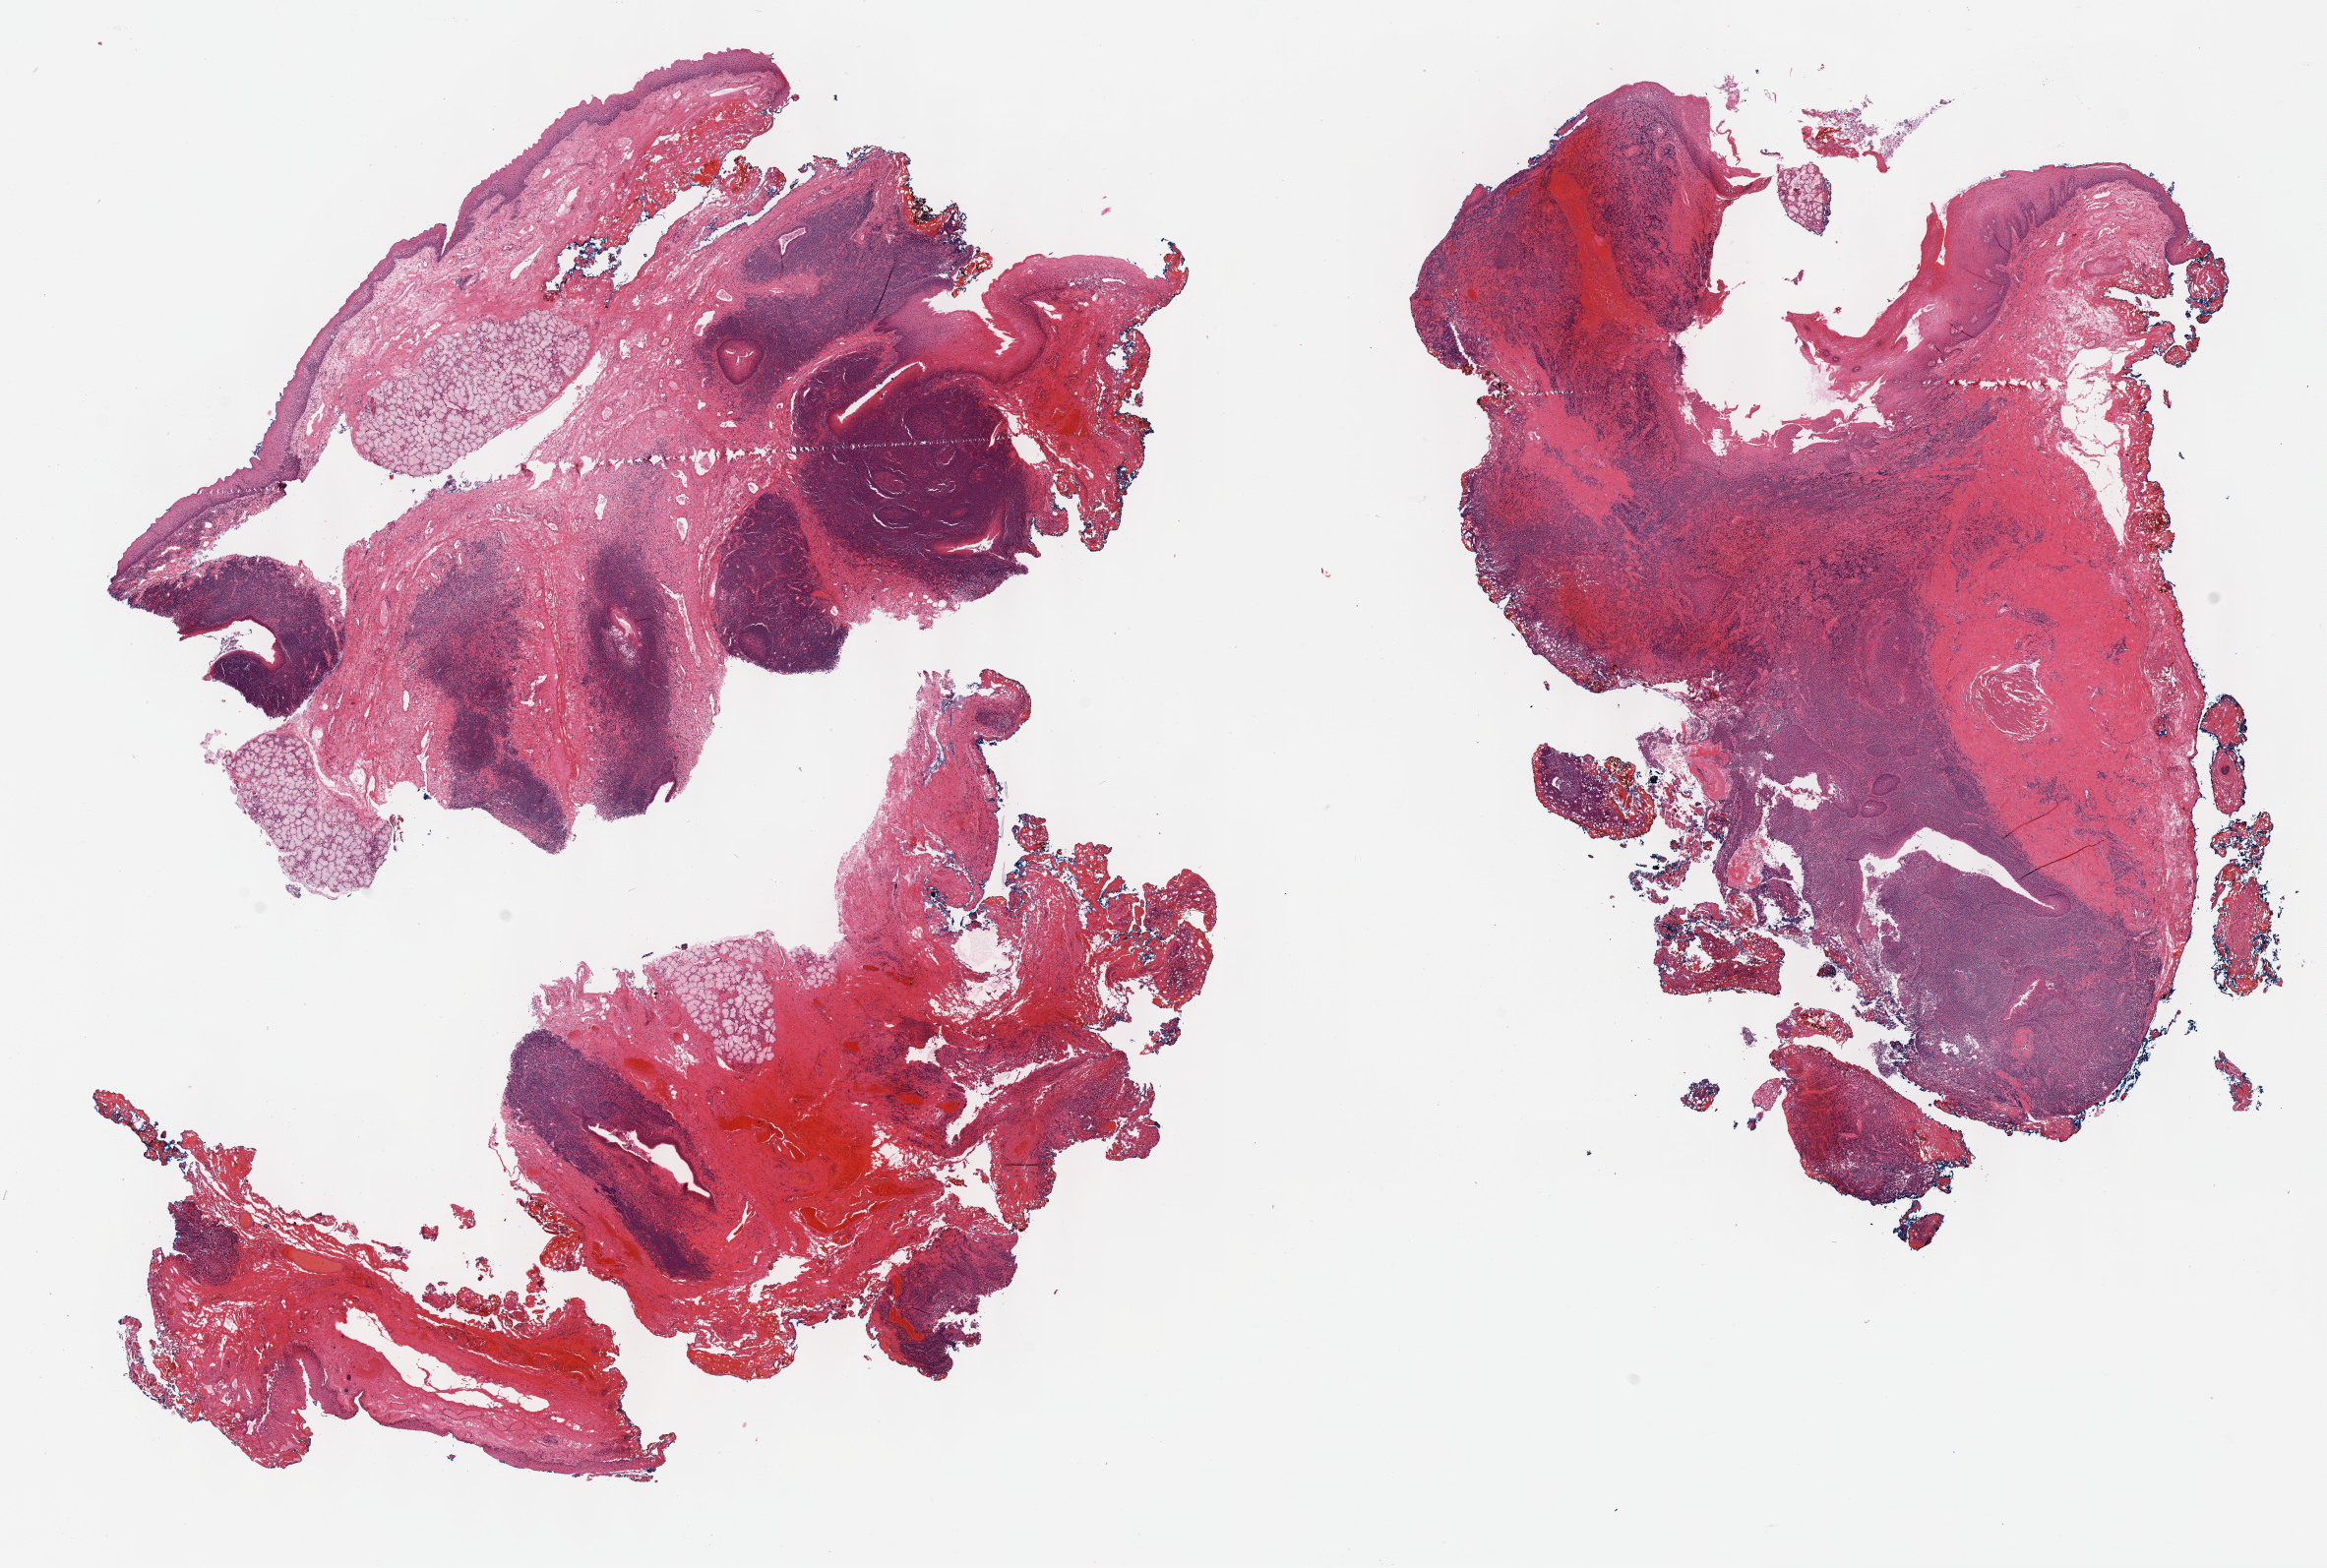
Digitized H&E tissue section (whole slide), a low-resolution overview of the entire scanned area, about 19.1 x 12.9 mm. Formalin-fixed paraffin-embedded (FFPE) diagnostic section. Head and neck, primary tumour sample. Male patient; age at initial diagnosis 49 years. Histologic grade: G2 (moderately differentiated).
• laterality: right
• histologic diagnosis: Squamous cell carcinoma, NOS (tonsil, NOS)